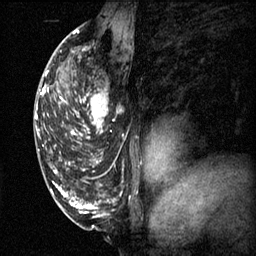
Breast MRI (dynamic contrast-enhanced), one sagittal slice; position 34 of 60 along the scan axis; 3 images stored at this slice position (order not interpretable as contrast timing); 1.5 T; TE 4.2 ms, TR 11.1 ms; 2 mm slice thickness; 256 × 256 image matrix, field of view 180 × 180 mm. Female patient, age 50 years.
Outlined on this slice (semi-automatically segmented with operator editing):
- analysis volume of interest (the breast-tissue region the enhancement analysis was run in; not a lesion): bounding box (x1, y1, x2, y2) in pixels: (68, 68, 117, 141)
- tumour enhancement mask (voxels above the 70 % enhancement threshold inside the analysis volume of interest): (71, 92, 109, 139)